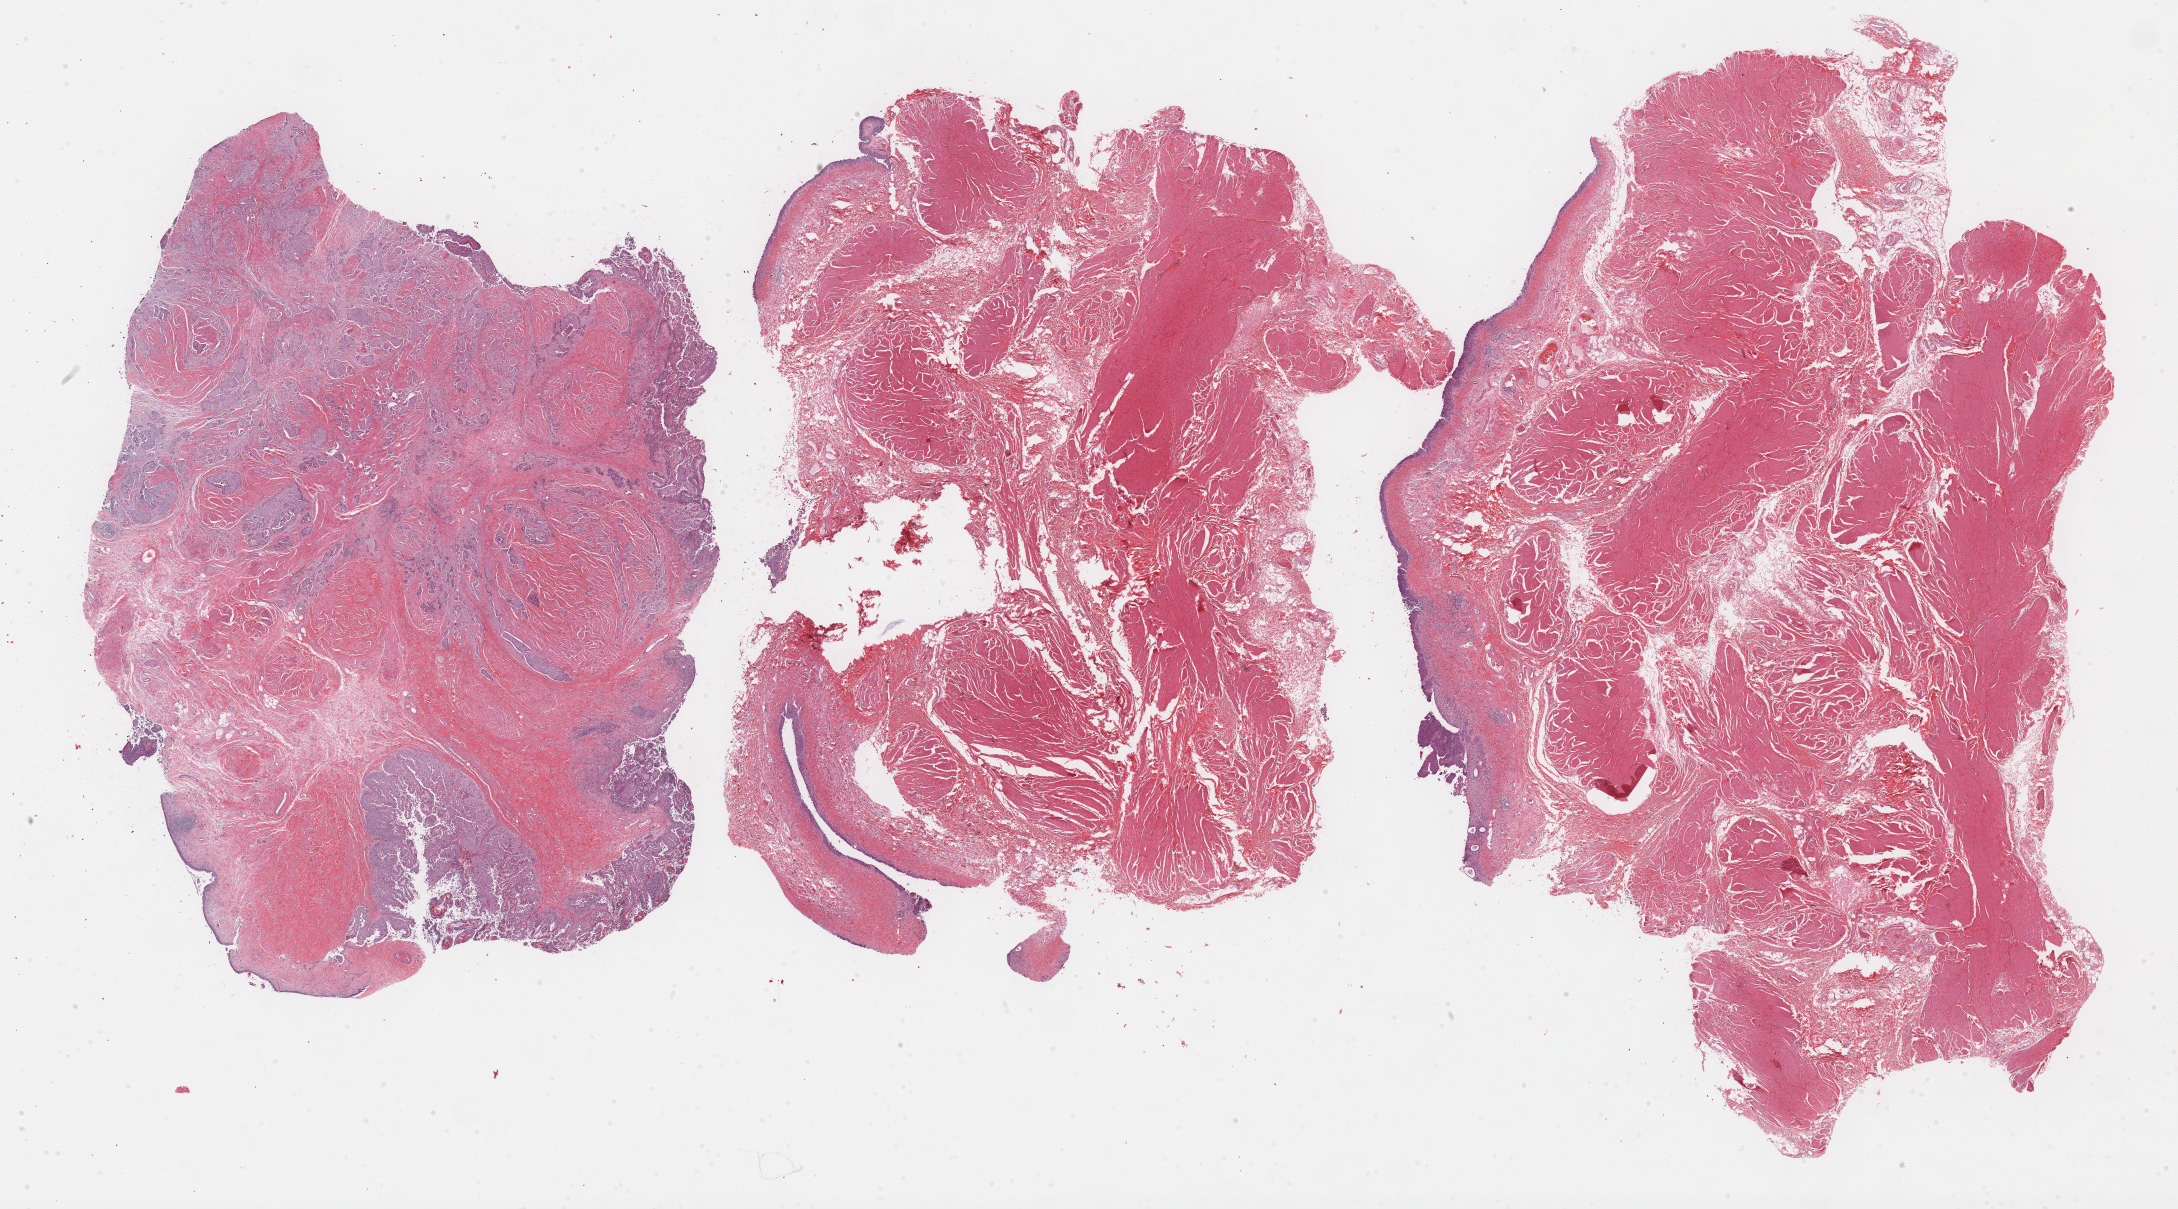
Whole-slide histology image, H&E-stained, a low-resolution overview of the entire scanned area, about 35.2 x 19.6 mm (from a 40x scan); FFPE section; primary tumour sample from the bladder. Male patient; age at initial diagnosis 82 years. Histologic grade: high grade.
* histologic diagnosis: Papillary transitional cell carcinoma
* AJCC pathologic stage: IV (6th edition)
* lymph nodes positive (case pathology): 5 of 93 examined